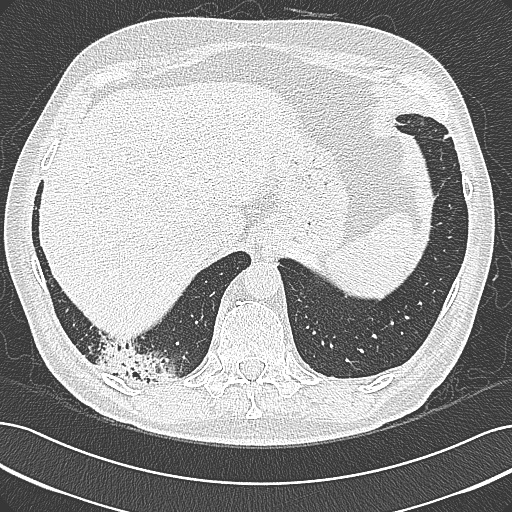
Chest CT (low-dose screening protocol), one axial image; first (baseline) screen; lung window (W 1500 / L -600 HU); 1 mm slice thickness; slice 252 of 355 in the series. Male, age 68 years at enrolment. Former smoker at enrolment.
Expert-annotated lung lesion, box from (x=94, y=337) to (x=192, y=398) px. Screening reader's record for this exam: no non-calcified nodule ≥4 mm recorded. Official screen result: negative screen, significant abnormalities not suspicious for lung cancer. Later outcome: lung cancer diagnosed 154 days after this screen — mucinous adenocarcinoma, right lower lobe, well differentiated (G1), stage IB (AJCC 6th edition), 50 mm at pathology.